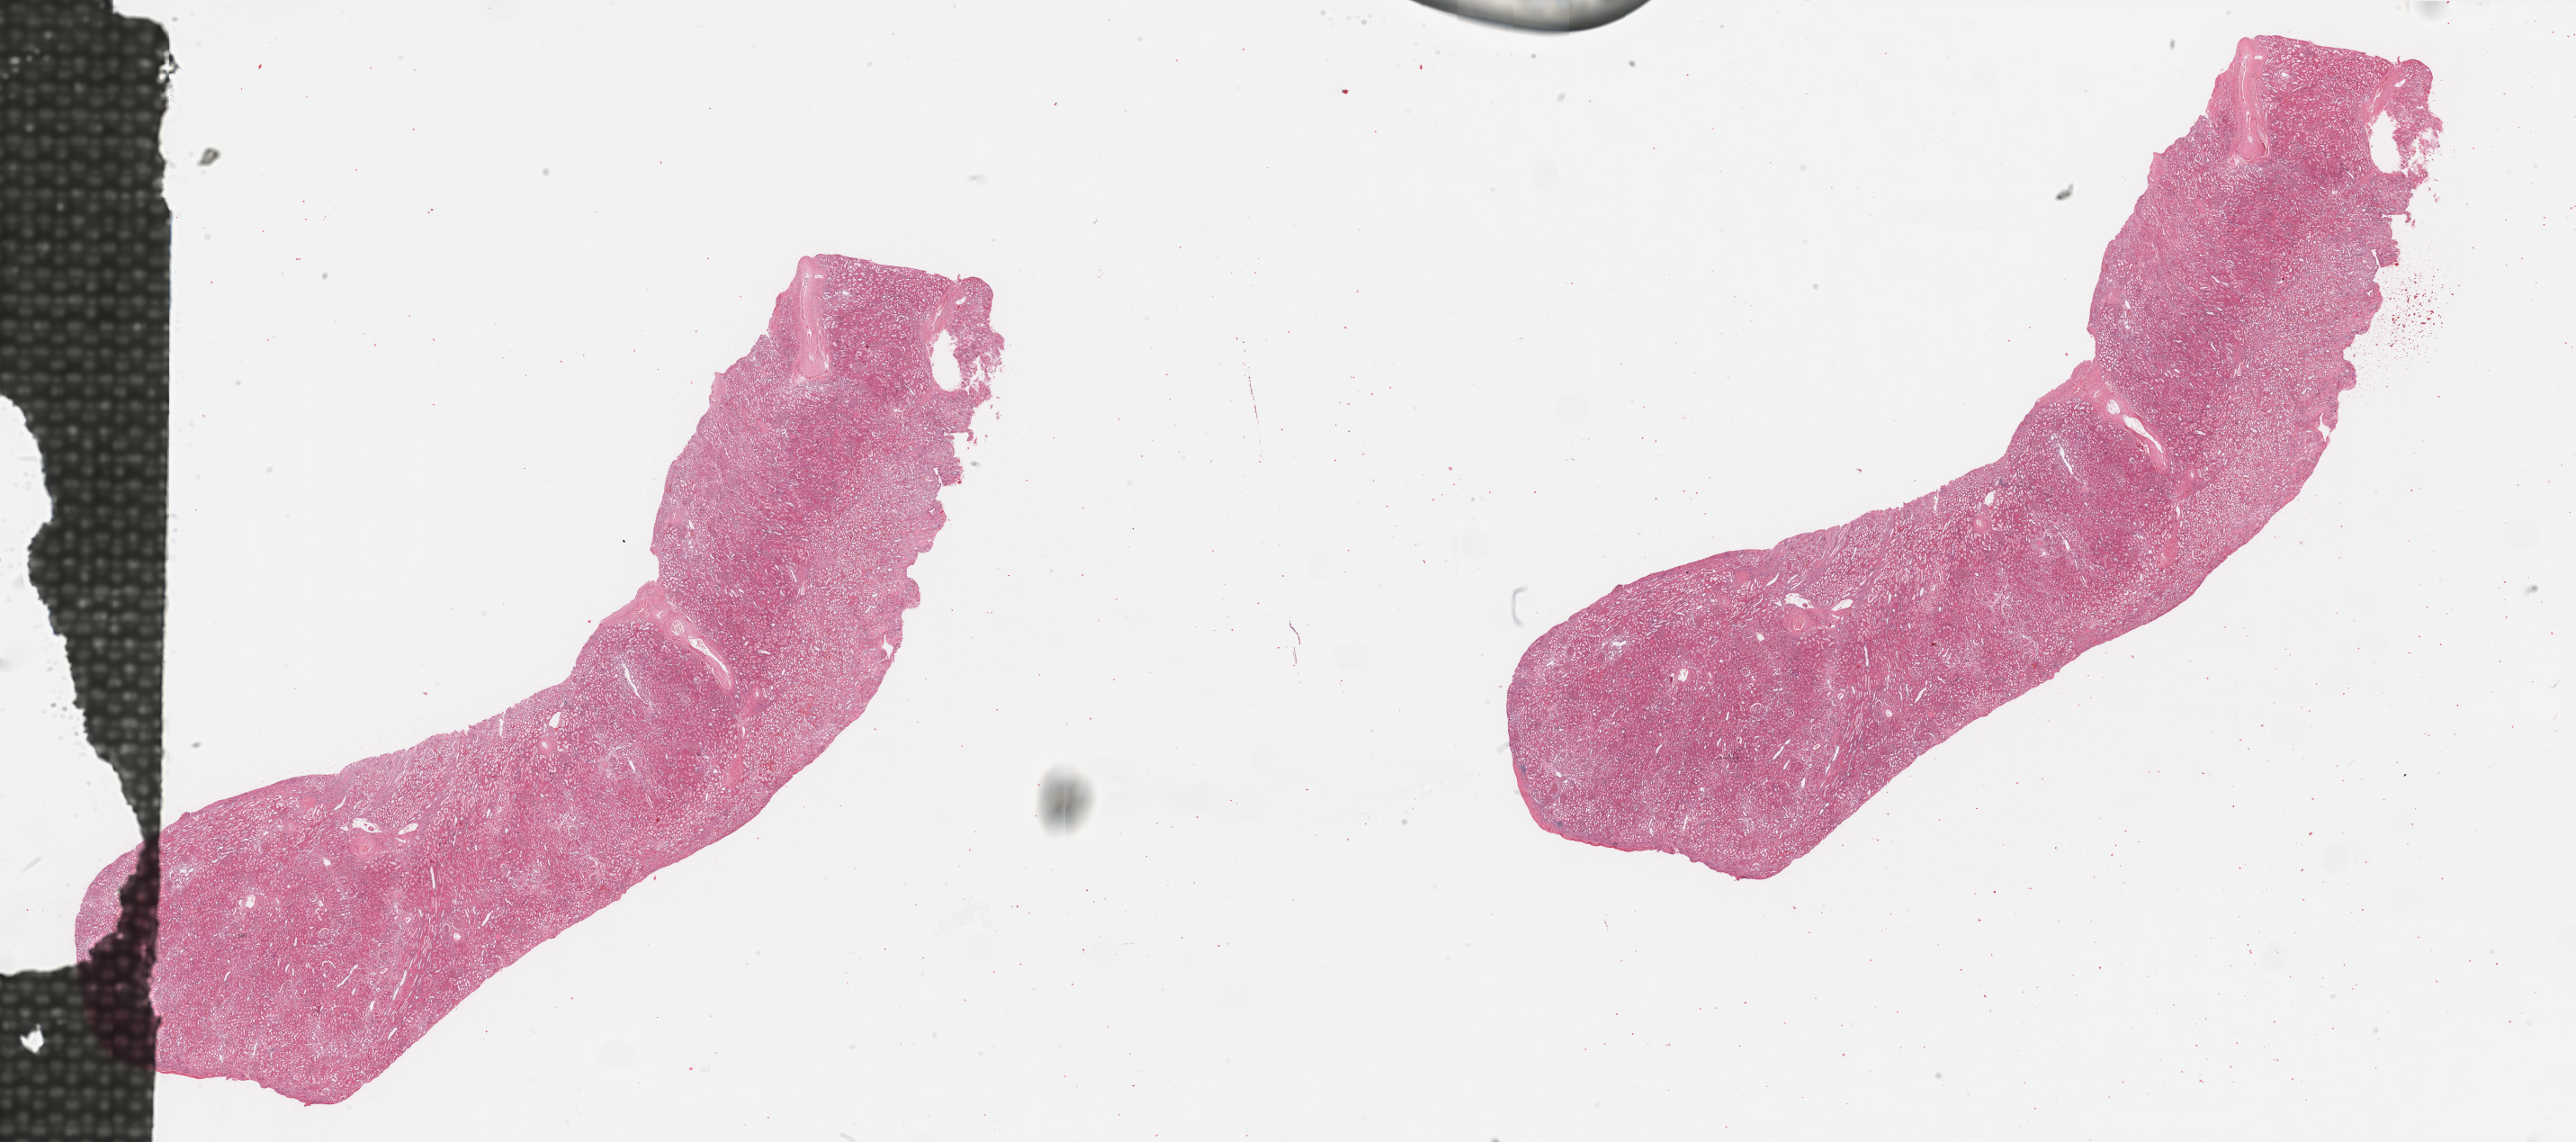
Digitized H&E-stained tissue section (whole slide), shown as a low-resolution overview of the whole scanned area (about 45.3 x 20.1 mm, slide scanned at 20x). Normal (non-tumour) tissue sample, sampled site: kidney. 66-year-old female patient.
- this section: normal (non-tumour) tissue from the same patient
- patient diagnosis: Renal cell carcinoma, NOS